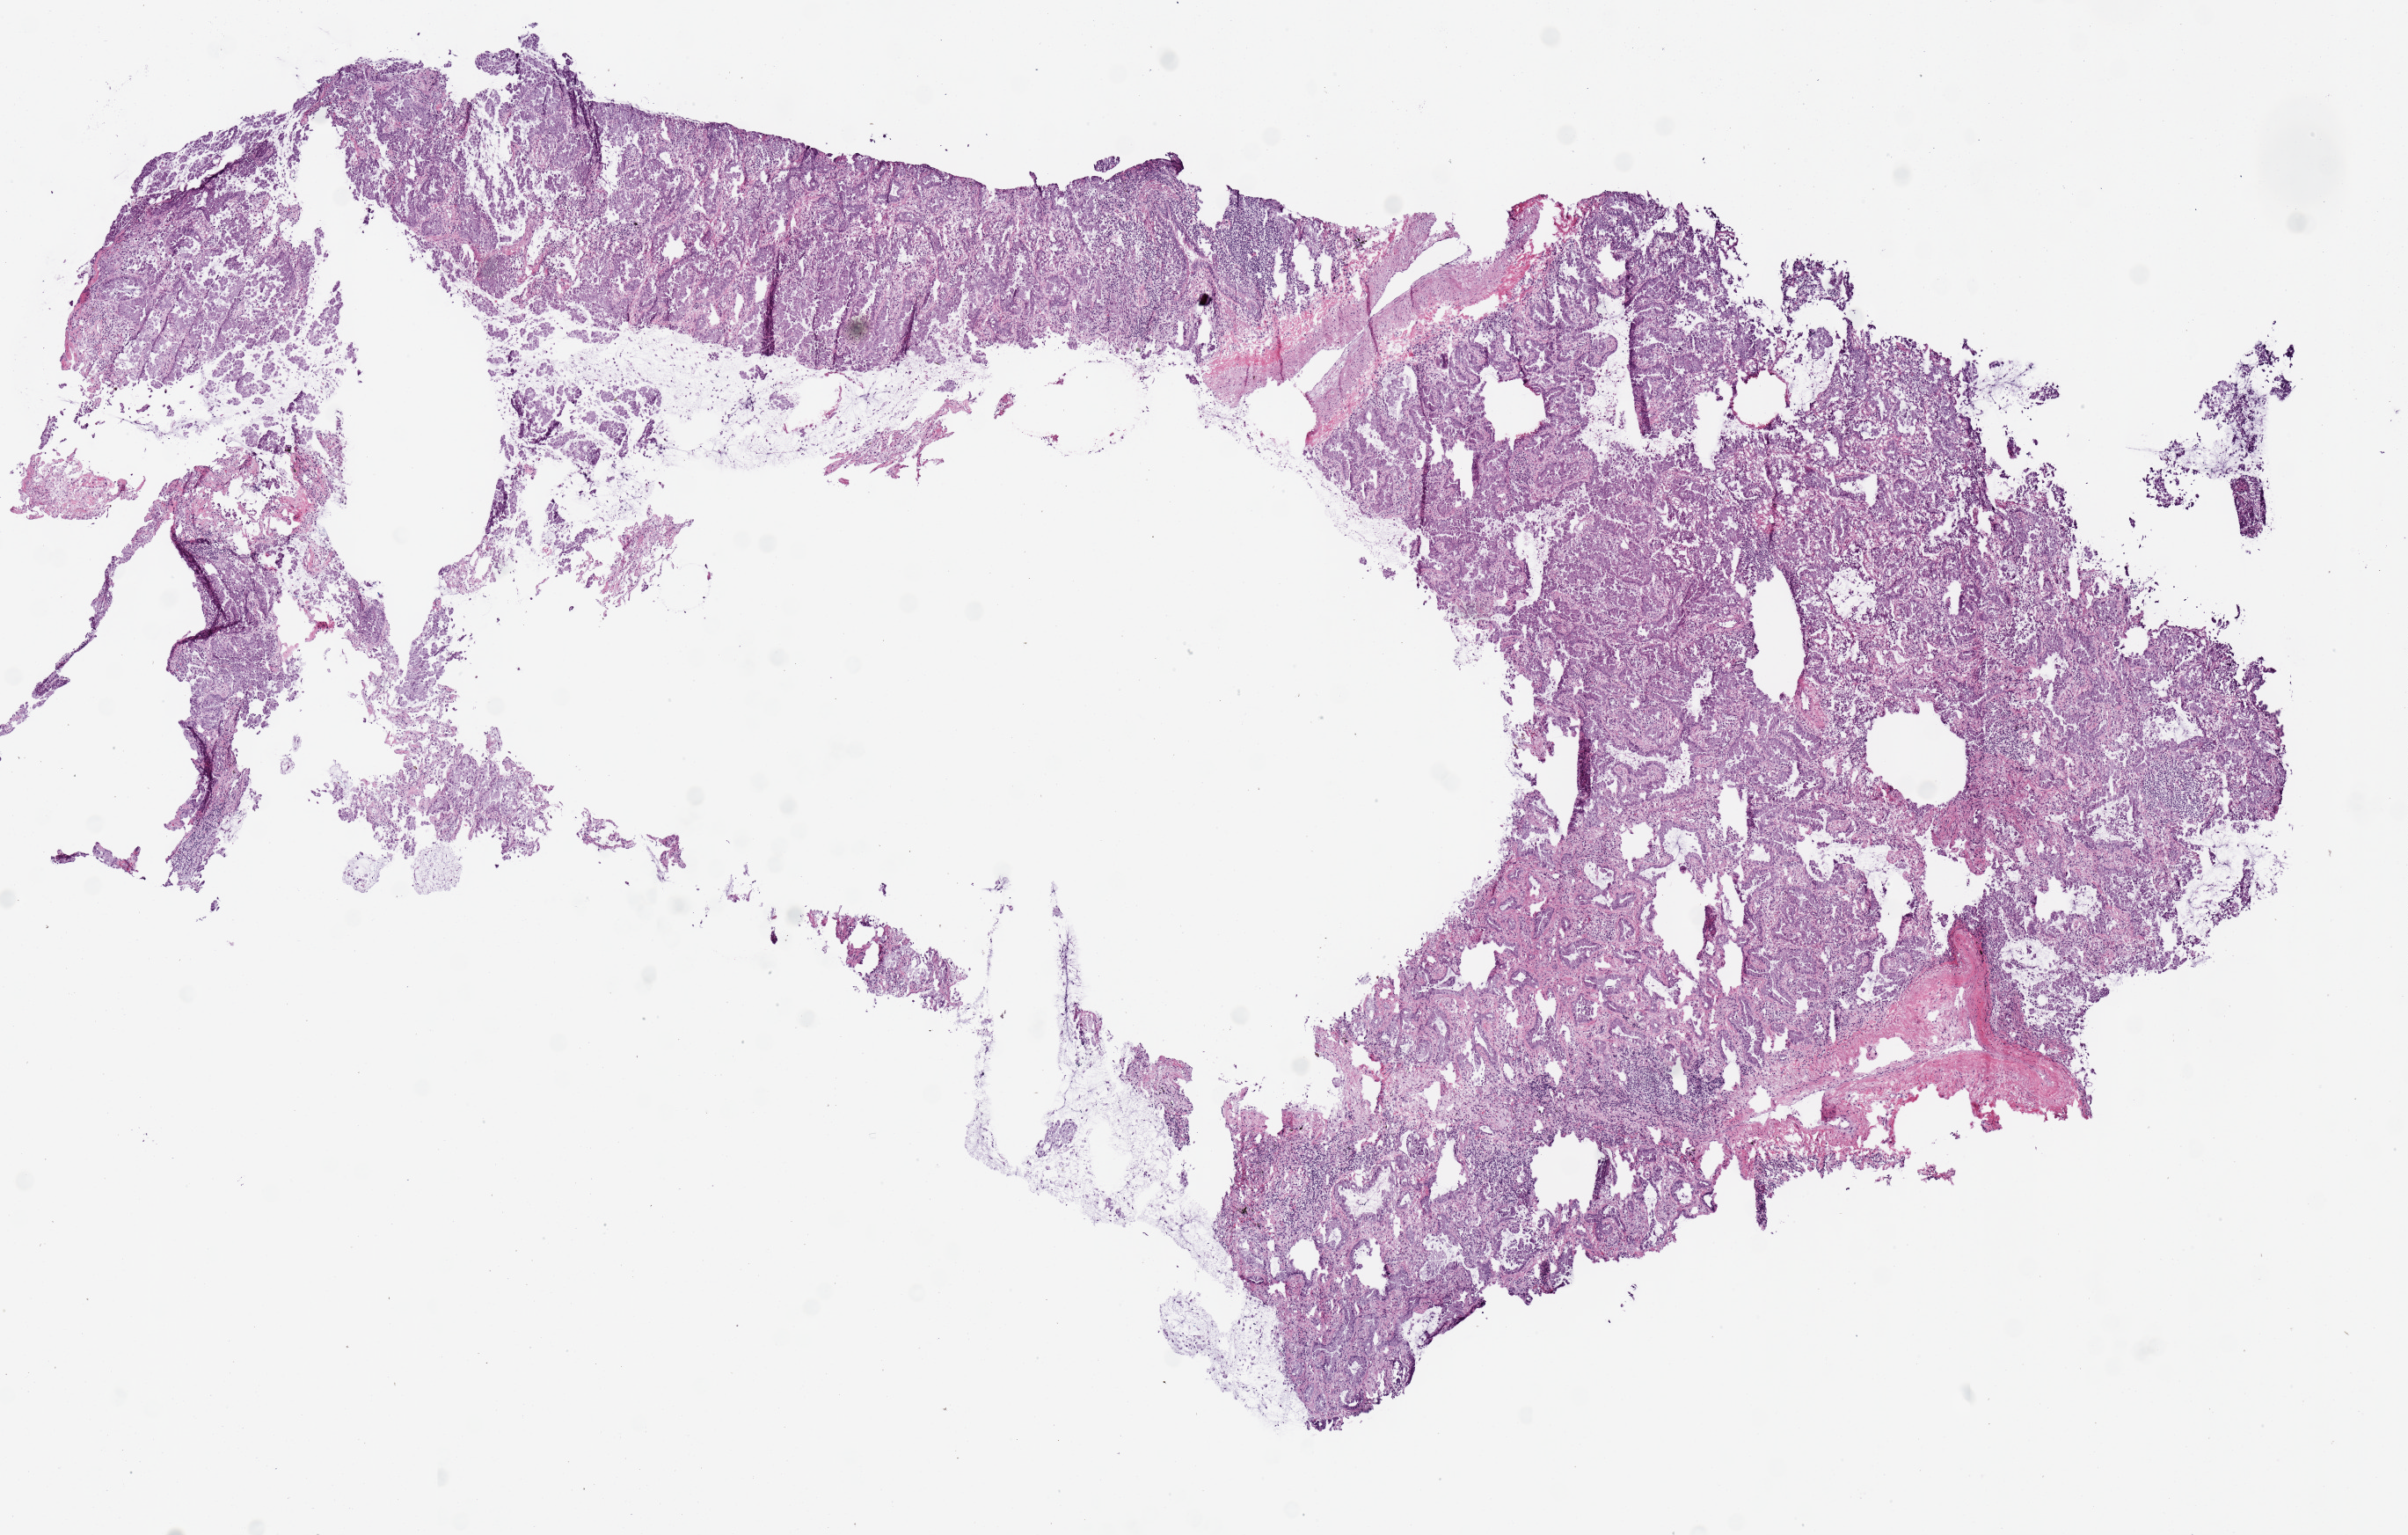
H&E-stained whole-slide image, a low-resolution overview of the entire scanned area, about 10.8 x 6.9 mm (slide scanned at 20x); frozen section; sample: primary tumour, lung. Female, age 59 years at initial diagnosis.
Histologic diagnosis: Adenocarcinoma with mixed subtypes (lower lobe, lung).